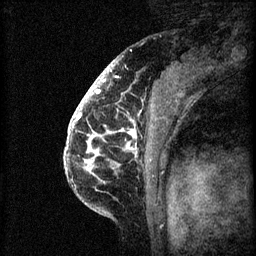
Breast MRI (dynamic contrast-enhanced), one sagittal slice. Slice 44 of 60 in the series (ordered by position). 3 images stored at this slice position (order not interpretable as contrast timing). 1.5 T. TE 4.2 ms, TR 8.2 ms. 2 mm slice thickness. 256 × 256 image matrix, field of view 180 × 180 mm. Female patient, age 41 years.
Outlined on this slice (semi-automatically segmented with operator editing):
- analysis volume of interest (the breast-tissue region the enhancement analysis was run in; not a lesion): bounding box (x1, y1, x2, y2) in pixels: (72, 108, 157, 205)
- tumour enhancement mask (voxels above the 70 % enhancement threshold inside the analysis volume of interest): (72, 108, 137, 173)